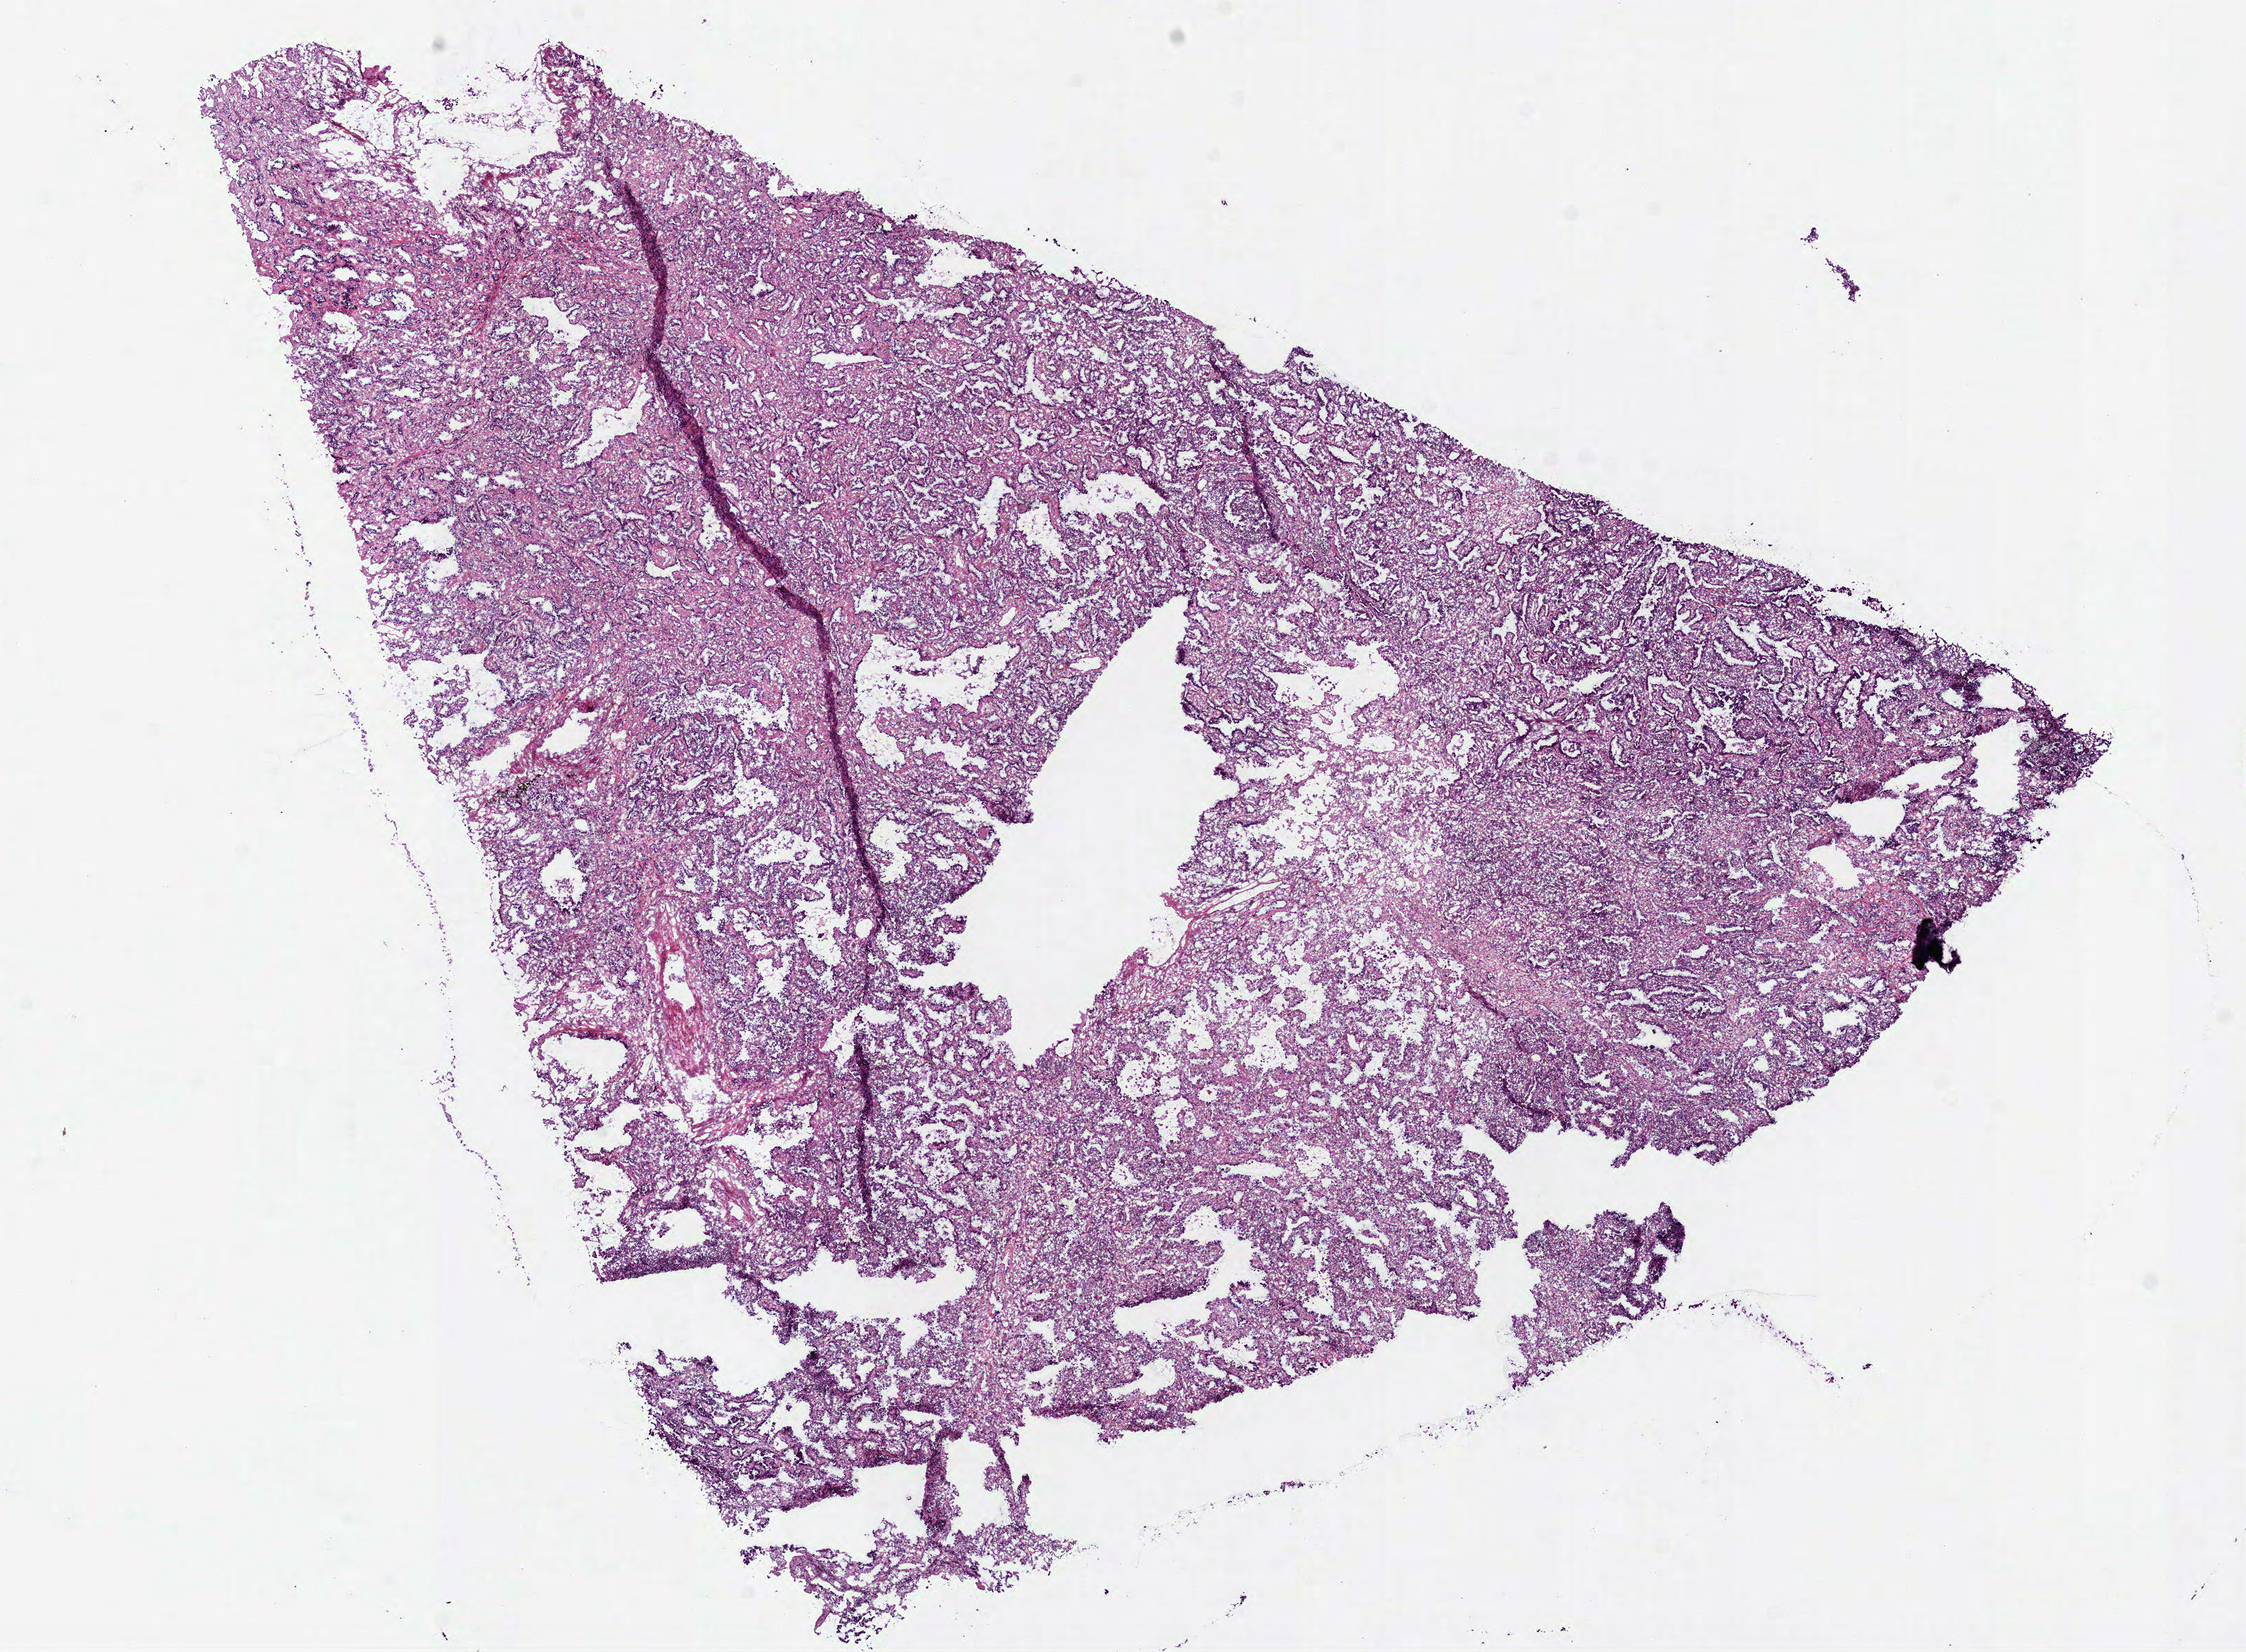
H&E whole-slide image — shown as a low-resolution overview of the whole scanned area (about 13.1 x 9.6 mm, slide scanned at 40x), frozen section from the bottom of the tissue portion, sample: primary tumour, lung. Female patient; age at initial diagnosis 86 years.
Histologic diagnosis: Adenocarcinoma, NOS (upper lobe, lung).